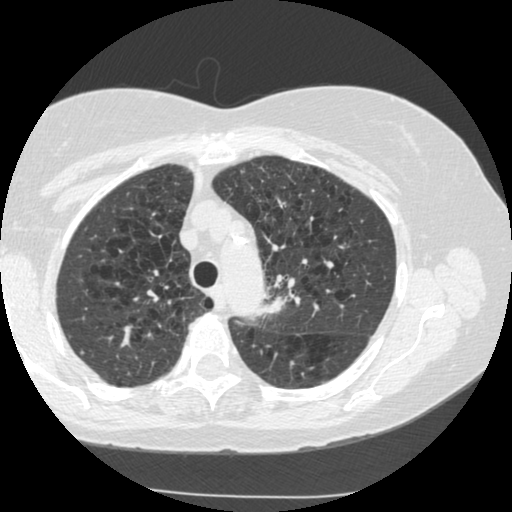
Axial slice from a low-dose chest CT screening exam, second annual screen, lung window (W 1500 / L -600 HU), standard (soft-tissue) reconstruction kernel (STANDARD), 120 kVp, slice 195 of 249 in the series. Female, age 70 years at enrolment.
• Lesion marked by an expert reader, bounding box [x1, y1, x2, y2] px = [237, 270, 299, 335].
• Reader record for this screening exam (exam-level; its link to the box is not recorded): non-calcified nodule or mass ≥4 mm, left upper lobe, 15 × 13 mm, spiculated (stellate) margins, soft tissue attenuation, pre-existing on the prior screen: yes; interval growth: yes.
• Official screen result: positive, other.
• Later outcome: lung cancer diagnosed 360 days after this screen — neoplasm, malignant, left upper lobe, stage IIIB (AJCC 6th edition), 40 mm at pathology.